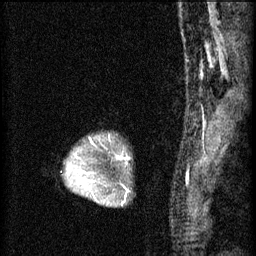
Breast MRI (dynamic contrast-enhanced), one sagittal slice; position 49 of 60 along the scan axis; 3 images stored at this slice position (order not interpretable as contrast timing); 1.5 T; TE 4.2 ms, TR 8.2 ms; 2 mm slice thickness; 256 × 256 image matrix, field of view 180 × 180 mm. Patient: female, 45 years.
Structures marked on this image (semi-automatic segmentation, software-assisted and operator-edited):
- analysis volume of interest (the breast-tissue region the enhancement analysis was run in; not a lesion): box from (x=62, y=136) to (x=129, y=205) px
- tumour enhancement mask (voxels above the 70 % enhancement threshold inside the analysis volume of interest): (x=76, y=138)–(x=127, y=203)